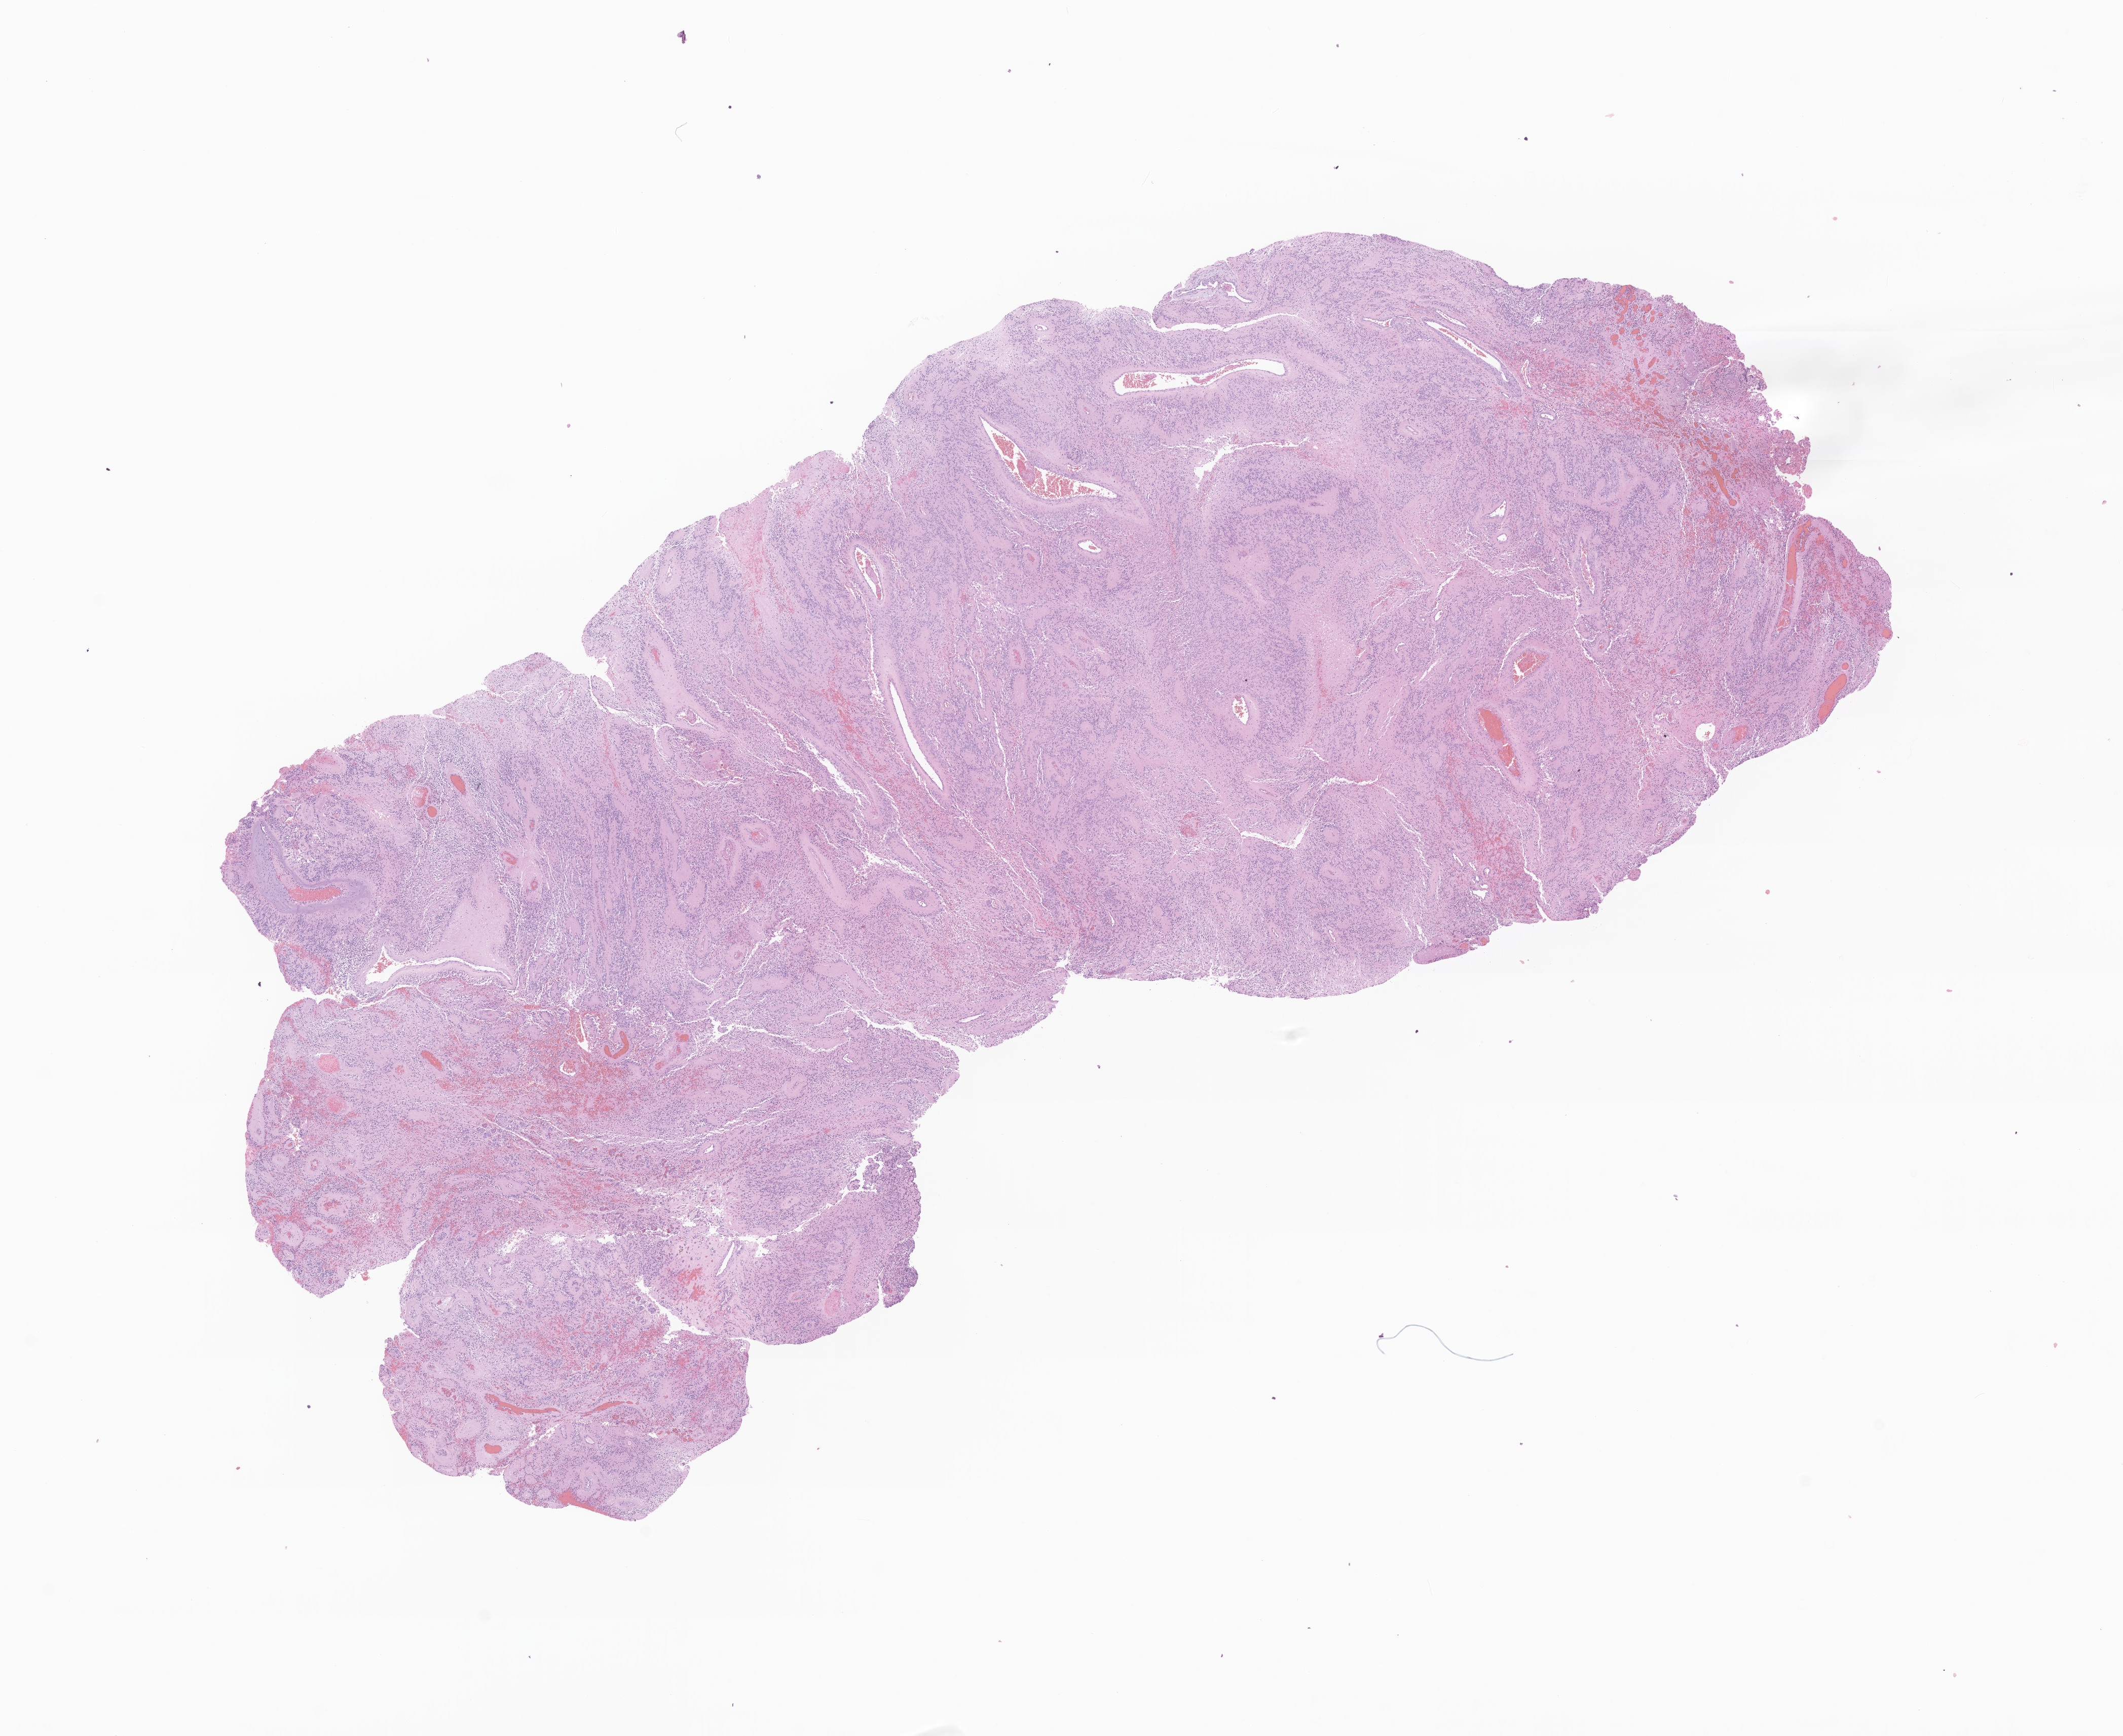
Whole-slide image, hematoxylin and eosin (H&E) stain of tumor tissue from the cerebellum, low-resolution overview of the scanned area, about 17.7 x 14.4 mm, FFPE section. Patient: male, age 54 months (4 years 6 months).
Recorded diagnosis: Ependymoma, NOS.